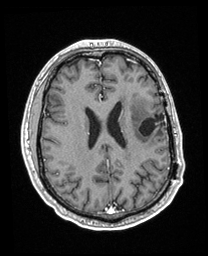
Brain MRI from a brain-tumour surgery series, one axial slice. Position 86 of 208 along the scan axis. T1-weighted post-contrast. 1 mm slice thickness. 208 × 256 image matrix. From the clinical record (not read from this slice): histopathology: Astrocytoma; WHO grade: 3; IDH mutation: yes; tumour location: Left Insular.
Outlined on this slice (manually delineated by an expert):
- previous resection cavity: box from (x=139, y=114) to (x=165, y=136) px